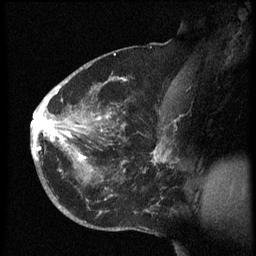
Breast MRI (dynamic contrast-enhanced), one sagittal slice; dynamic contrast-enhanced series, image 2 of 3 at this slice position (ordered by acquisition); 1.5 T; TE 4.2 ms, TR 8.4 ms; 256 × 256 image matrix, field of view 200 × 200 mm. Female patient, age 38 years. Case-level facts recorded for this patient, not image findings: setting: breast cancer imaged before/during neoadjuvant chemotherapy; receptor status: HER2-positive.
Outlined on this slice (semi-automatically segmented with operator editing):
- analysis volume of interest (the breast-tissue region the enhancement analysis was run in; not a lesion): bounding box <32,74,173,202> (left, top, right, bottom; pixels)
- tumour enhancement mask (voxels above the 70 % enhancement threshold inside the analysis volume of interest): <32,78,170,201>